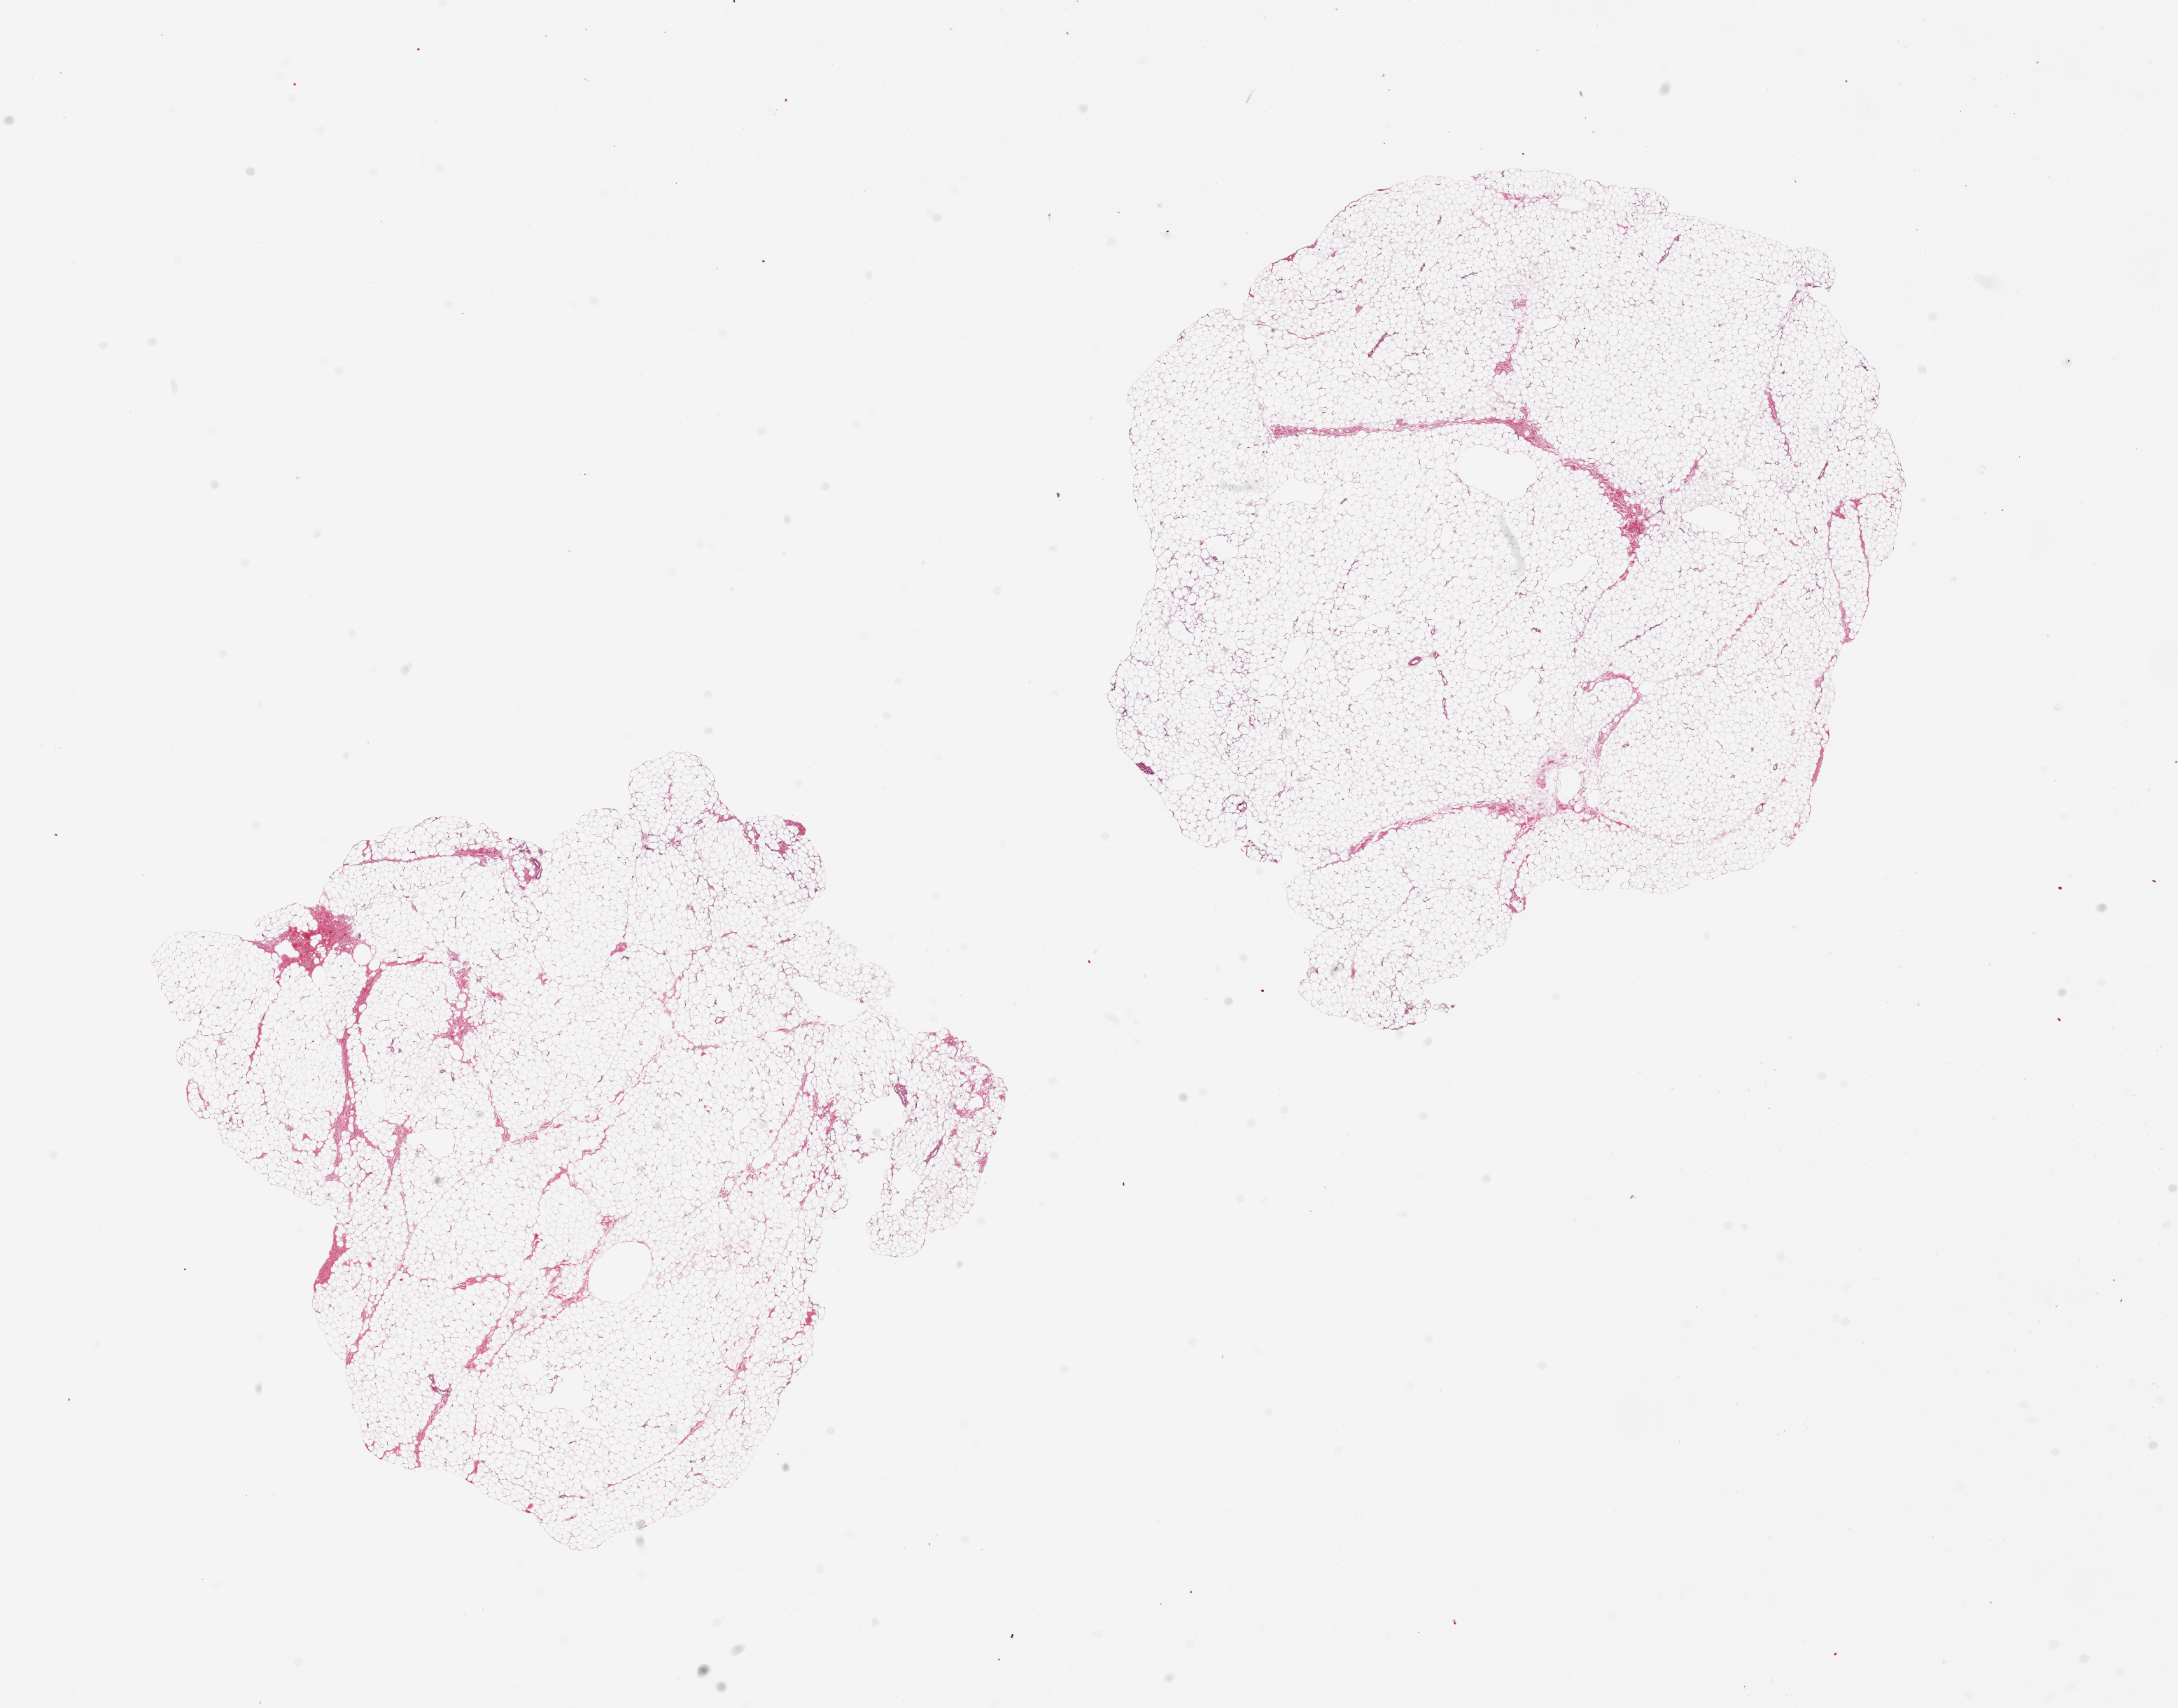
Whole-slide image, hematoxylin and eosin (H&E) stain, brightfield, low-resolution overview of the scanned area, about 24.6 x 19.3 mm (slide scanned at 20x); PAXgene-fixed, paraffin-embedded tissue; sampled site (target tissue): breast; donor tissue sample. Donor sex: male.
Reviewer comment on this tissue sample: 2 pieces, 9x8 and 9x8.5mm; no ductal elements, all adipose, trace fibrous tissue.